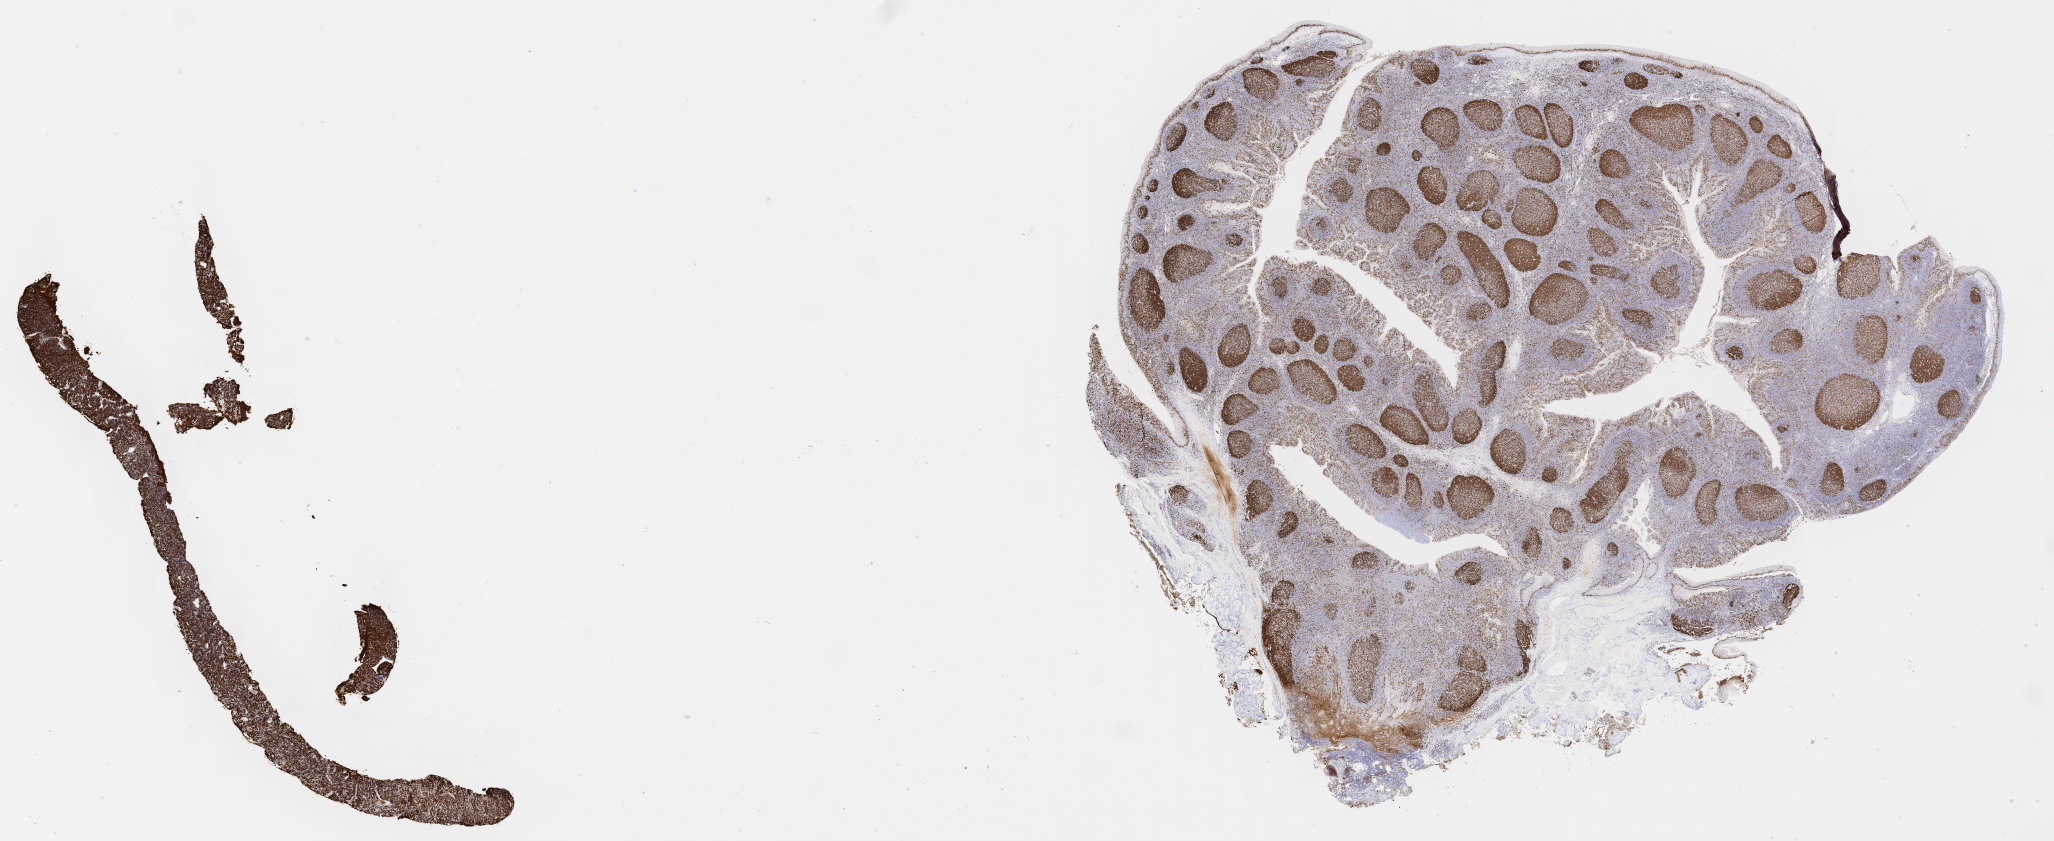
Immunohistochemistry (IHC) whole-slide image stained for Ki-67, whole scanned area (about 33.2 x 13.6 mm) shown as a low-resolution overview; specimen: tumor tissue; site: ovary. Female, age 9 years at initial diagnosis.
• diagnosis: Burkitt lymphoma, NOS